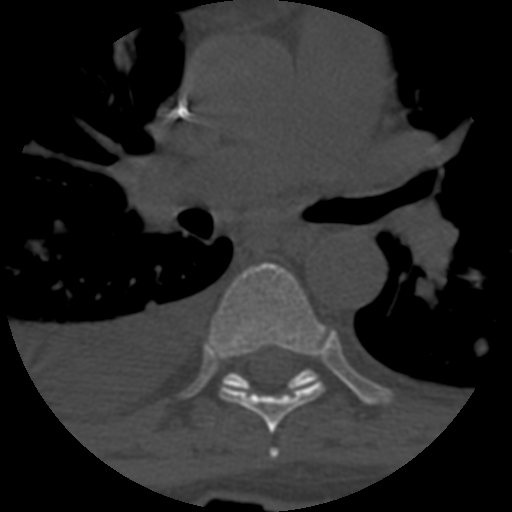
CT including the spine, one axial slice; slice 430 of 708 in the series (ordered by position); reconstruction kernel STANDARD; 120 kVp; one of 3 acquisitions stored at this slice position; bone window (W 1800 / L 400 HU); 512 × 512 image matrix, field of view 160 × 160 mm. Patient age 55 years. Case-level facts recorded for this patient, not image findings: primary cancer: colon; vertebrae with lytic lesions (as recorded): T12, L1, L5.
Annotated regions visible in this slice (semi-automatic segmentation, software-assisted and operator-edited):
- T5 vertebra: box from (x=269, y=448) to (x=279, y=459) px
- T6 vertebra: (x=210, y=262)–(x=323, y=433)
- T7 vertebra: (x=222, y=369)–(x=317, y=389)